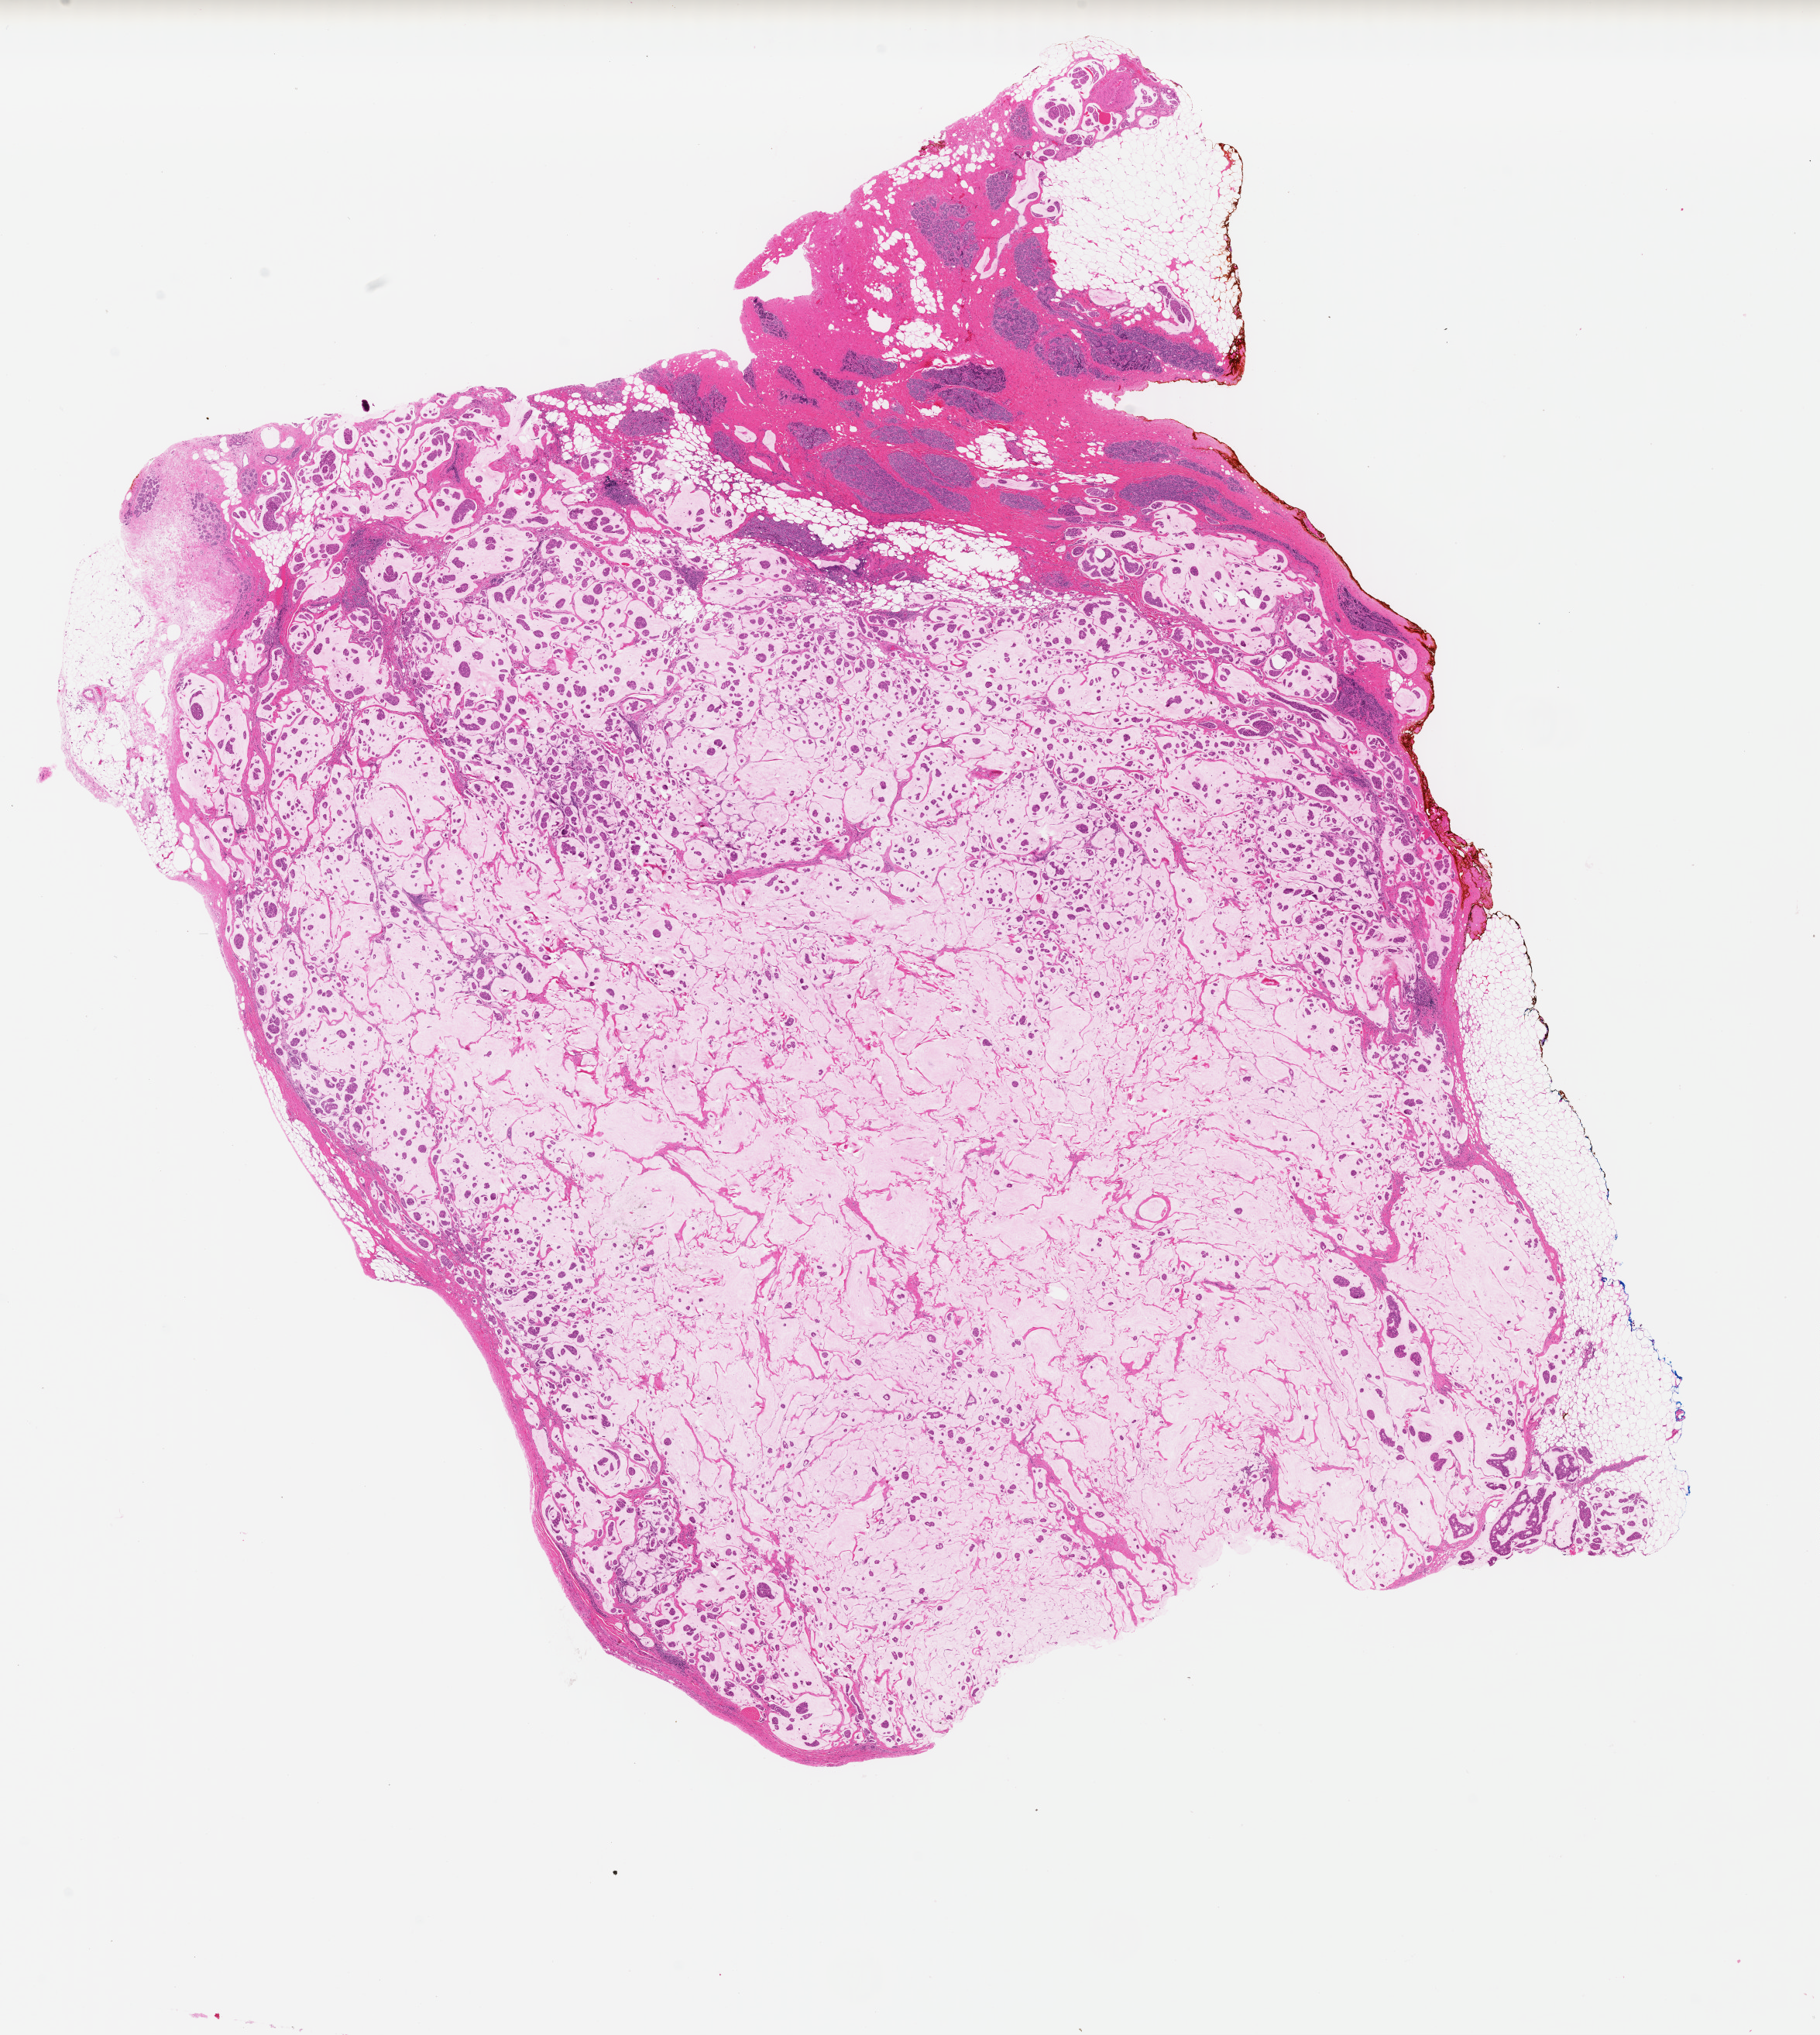
Digitized H&E-stained tissue section (whole slide) — shown as a low-resolution overview of the whole scanned area (about 18.5 x 20.6 mm, slide scanned at 40x). Formalin-fixed paraffin-embedded (FFPE) diagnostic section. Primary tumour sample from the breast. Female patient; age at initial diagnosis 47 years.
Histologic diagnosis: Mucinous adenocarcinoma.